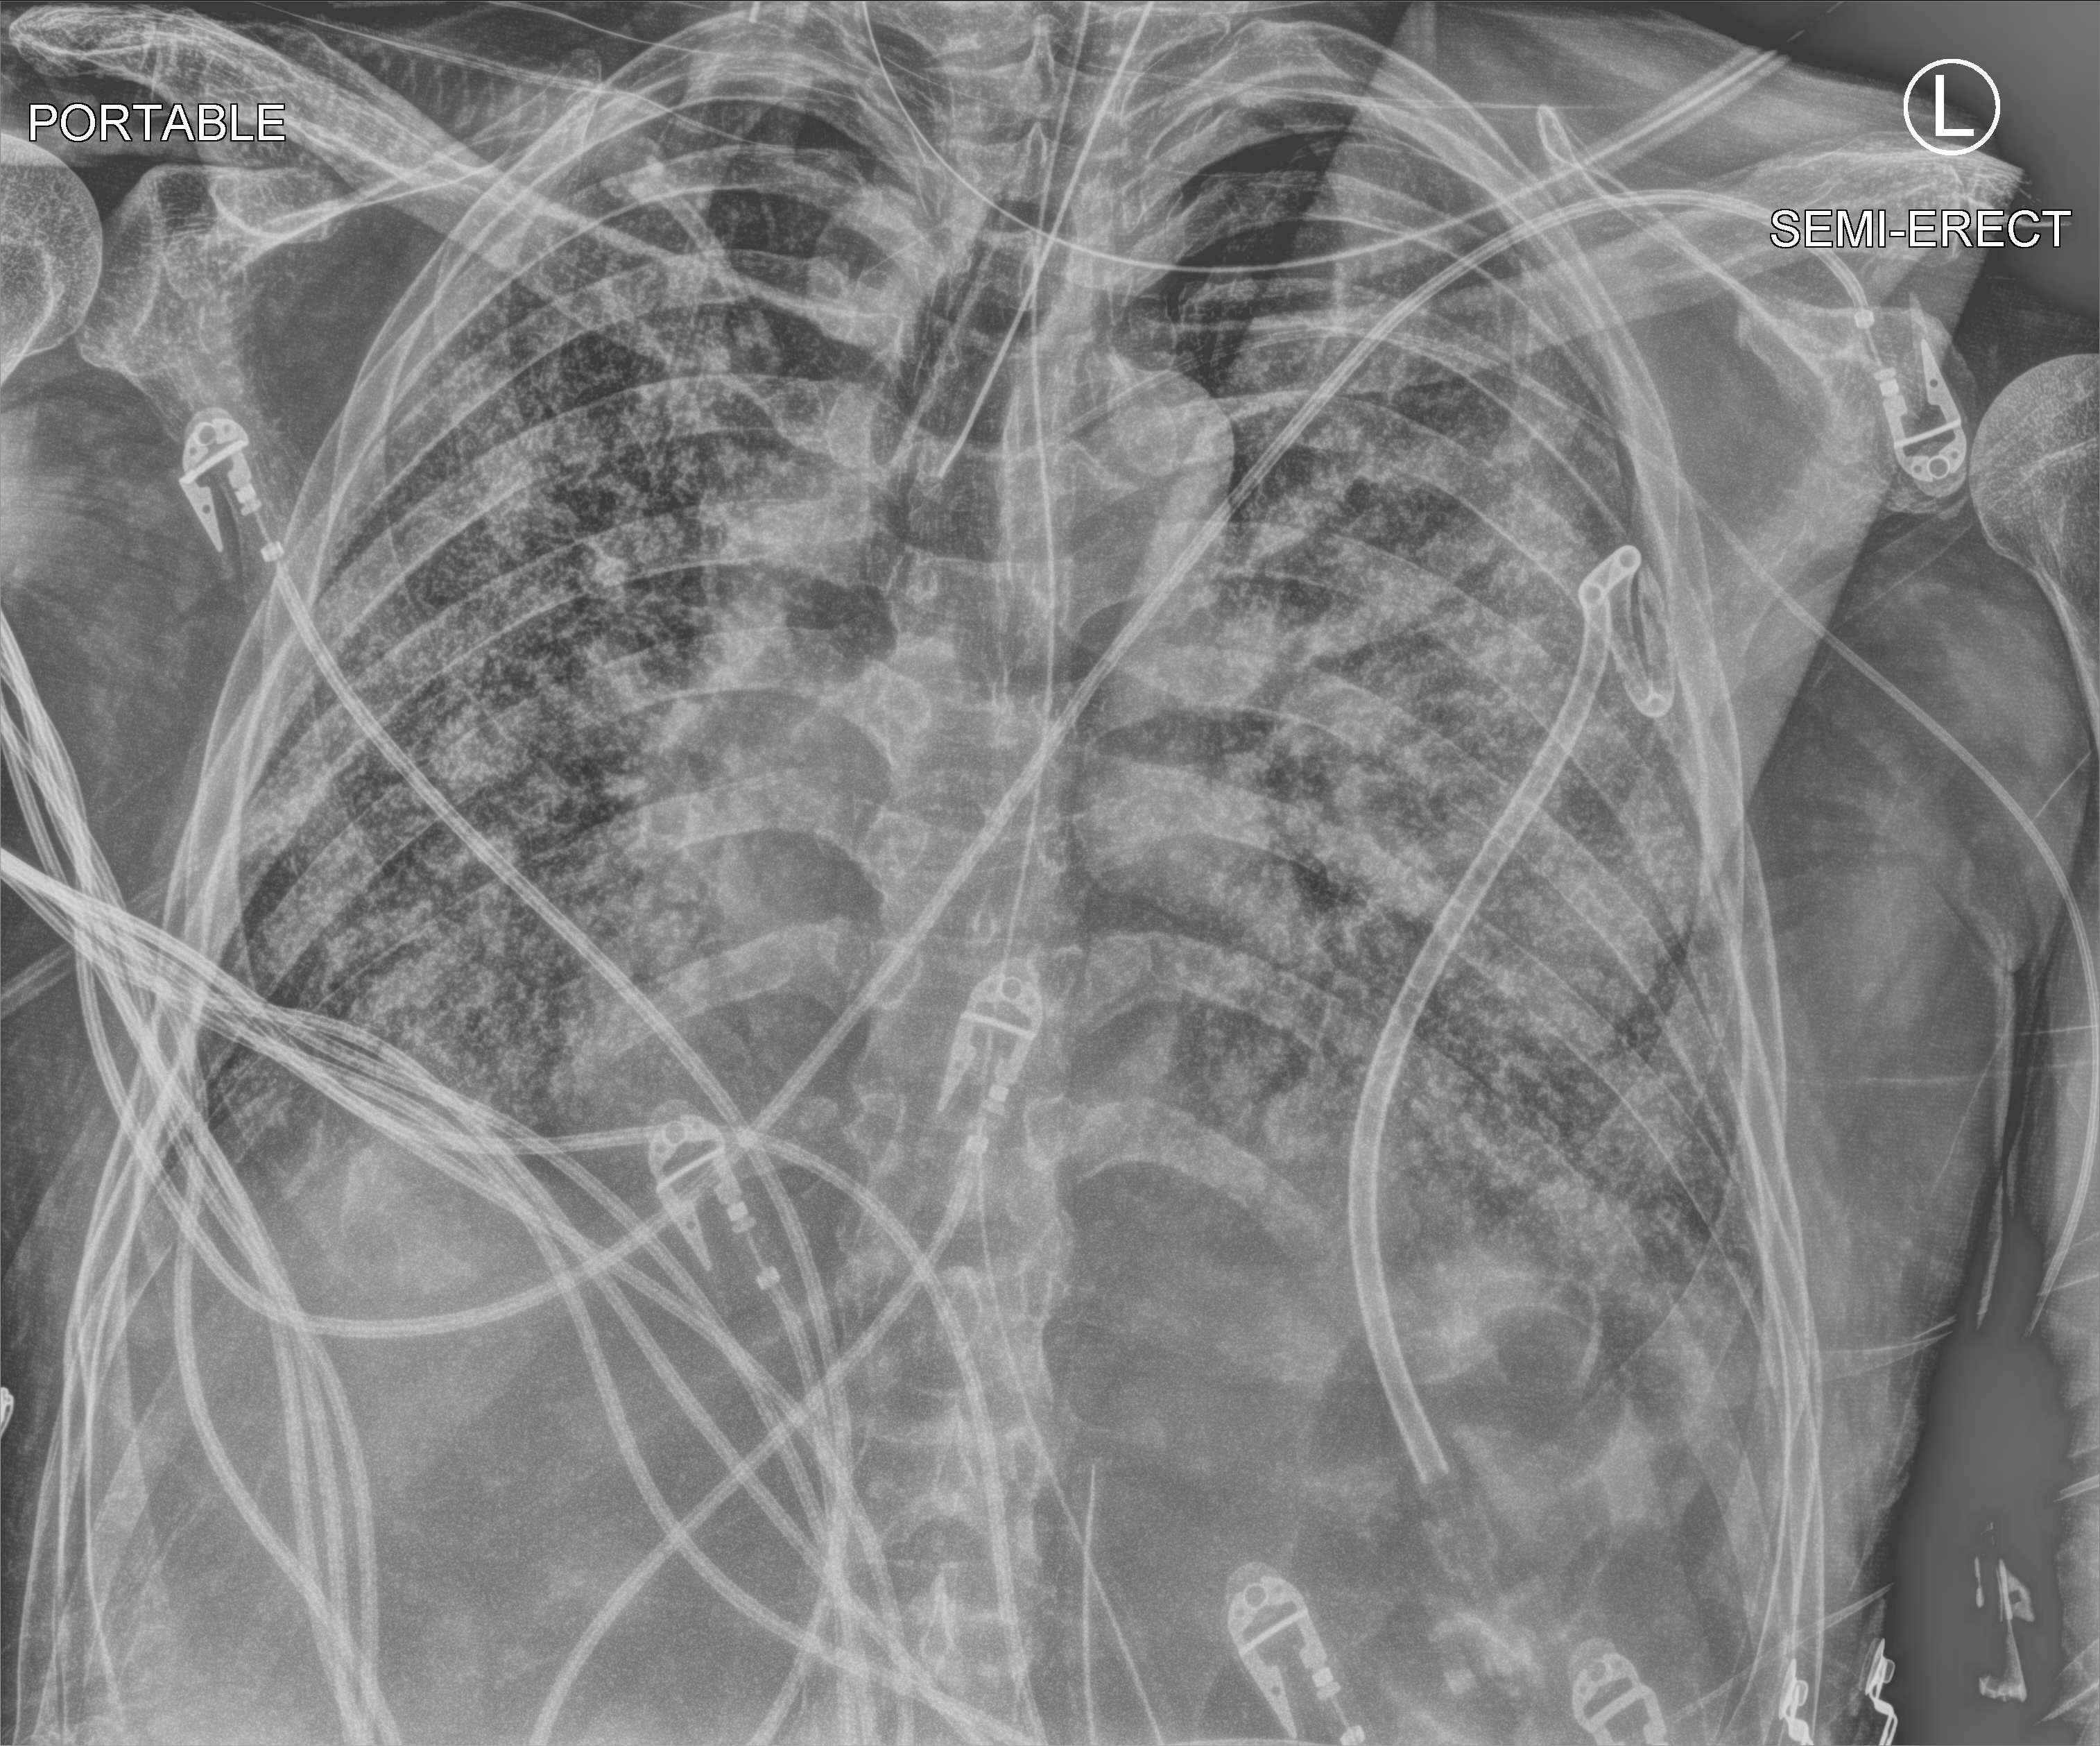
Portable chest radiograph, anteroposterior (AP) projection. Patient hospitalised with COVID-19; male, aged 60–74 years.
Admission-level facts for this patient (not findings on this image; timing relative to this image not recorded): length of hospital stay: 54 days; mechanically ventilated during this hospital stay: yes; admitted to intensive care during this hospital stay: yes.